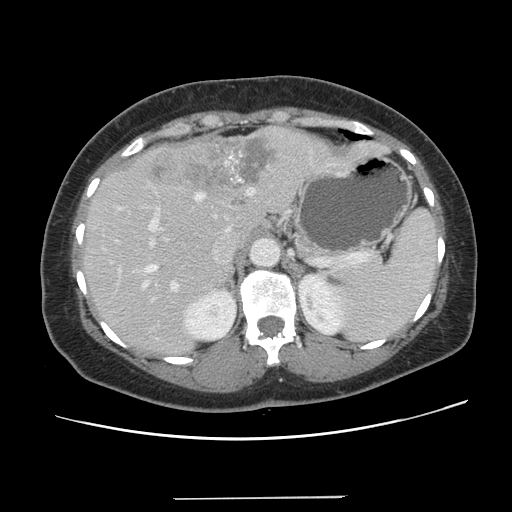
Contrast-enhanced abdominal CT, one axial slice; slice 92 of 141 in the series (ordered by position); 120 kVp; intravenous contrast given; soft-tissue window (W 400 / L 40 HU); 2.5 mm slice thickness; 512 × 512 image matrix, field of view 366 × 366 mm. Female patient, age 53 years. Case-level facts recorded for this patient, not image findings: diagnosis: colorectal cancer liver metastases, imaged before liver resection.
Structures marked on this image (outlined manually by an expert reader):
- hepatic veins: bounding box [x1, y1, x2, y2] px = [142, 193, 202, 287]
- liver: [85, 128, 384, 354]
- planned liver remnant (the part of the liver to remain after resection): [84, 209, 263, 354]
- portal vein (with intrahepatic branches): [148, 189, 253, 292]
- liver metastasis: [148, 137, 274, 190]